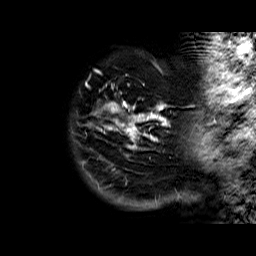
Breast MRI (dynamic contrast-enhanced), one sagittal slice. Position 5 of 60 along the scan axis. Dynamic contrast-enhanced series, time point 2 of 6 at this slice position (early post-contrast). 1.5 T. TE 6.3 ms, TR 32.4 ms. 256 × 256 image matrix, field of view 200 × 200 mm. Female patient. Case-level facts recorded for this patient, not image findings: setting: breast cancer imaged before/during neoadjuvant chemotherapy; receptor status: HR-positive, HER2-negative.
Outlined on this slice (semi-automatically segmented with operator editing):
- analysis volume of interest (the breast-tissue region the enhancement analysis was run in; not a lesion): bounding box [x1, y1, x2, y2] px = [78, 72, 176, 183]
- tumour enhancement mask (voxels above the 100 % enhancement threshold inside the analysis volume of interest): [86, 72, 167, 149]